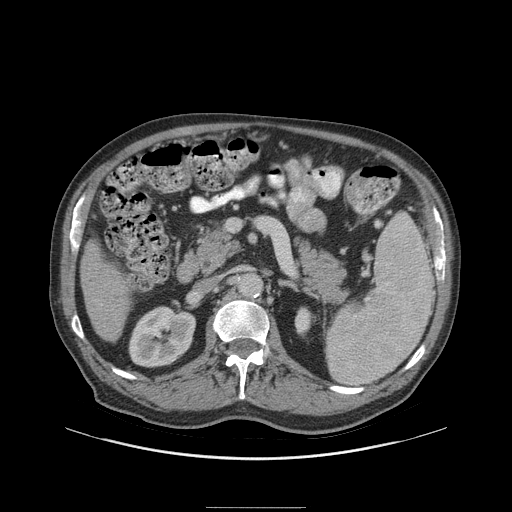
Contrast-enhanced abdominal CT (liver protocol), one axial slice; position 35 of 105 along the scan axis; reconstruction kernel STANDARD; soft-tissue window (W 400 / L 40 HU); 512 × 512 image matrix, field of view 440 × 440 mm. From the clinical record (not read from this slice): diagnosis: hepatocellular carcinoma (patient treated with transarterial chemoembolisation; whether this scan precedes or follows treatment is not stated here); TNM stage (as recorded): Stage-I; Child-Pugh class: A.
Outlined on this slice (semi-automatically segmented with operator editing):
- liver parenchyma outside the tumour (the mass and vessels are separate outlines, so this box may not span the whole liver): box from (x=80, y=240) to (x=130, y=342) px